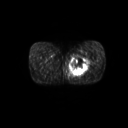
FDG PET of an extremity soft-tissue mass (from a PET/CT study), one axial slice; slice 26 of 267 in the series (ordered by position); 3.27 mm slice thickness; 128 × 128 image matrix, field of view 600 × 600 mm. Male patient, age 59 years. Case-level facts recorded for this patient, not image findings: histological type: pleiomorphic liposarcoma; grade: high; site of the primary tumour: left thigh.
Structures marked on this image (expert contour drawn on MRI and transferred to this co-registered scan by the dataset authors):
- gross tumour volume including surrounding oedema: box from (x=70, y=55) to (x=91, y=77) px
- gross tumour volume (mass): (x=71, y=56)–(x=89, y=75)